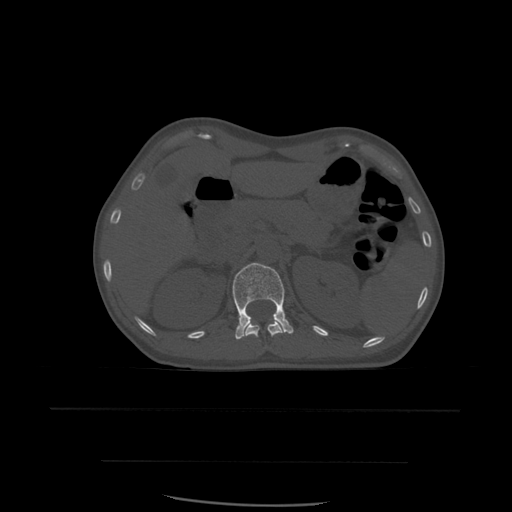
CT including the spine, one axial slice; slice 258 of 574 in the series (ordered by position); bone window (W 1800 / L 400 HU); 512 × 512 image matrix. Patient age 48 years. Case-level facts recorded for this patient, not image findings: primary cancer: lung.
Structures marked on this image (semi-automatically segmented with operator editing):
- L1 vertebra: bounding box [x1, y1, x2, y2] px = [233, 263, 294, 340]
- T12 vertebra: [244, 321, 284, 339]